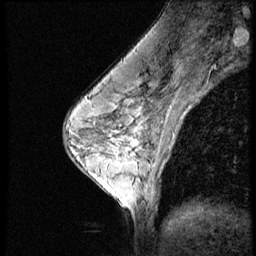
Breast MRI (dynamic contrast-enhanced), one sagittal slice. Slice 33 of 52 in the series (ordered by position). 3 images stored at this slice position (order not interpretable as contrast timing). 1.5 T. TE 4.2 ms, TR 9 ms. 2.5 mm slice thickness. 256 × 256 image matrix. Patient: female, 50 years. From the clinical record (not read from this slice): setting: breast cancer imaged before/during neoadjuvant chemotherapy; receptor status: HR-positive, HER2-negative.
Annotated regions visible in this slice (semi-automatically segmented with operator editing):
- analysis volume of interest (the breast-tissue region the enhancement analysis was run in; not a lesion): box from (x=103, y=130) to (x=151, y=181) px
- tumour enhancement mask (voxels above the 140 % enhancement threshold inside the analysis volume of interest): (x=133, y=141)–(x=138, y=147)